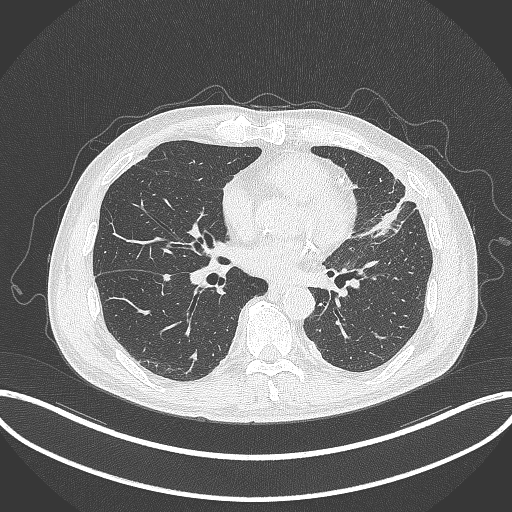
Chest CT, one axial slice; position 147 of 382 along the scan axis; reconstruction kernel B70f; lung window (W 1500 / L -600 HU); 1 mm slice thickness; 512 × 512 image matrix, field of view 415 × 415 mm. Male patient, age 64 years. Case-level facts recorded for this patient, not image findings: clinical TNM (as recorded): T4 N1 M0.
Annotated regions visible in this slice (rectangle marked by the reading radiologist):
- lung tumour (recorded histology: adenocarcinoma): bounding box (x1, y1, x2, y2) in pixels: (363, 189, 419, 239)